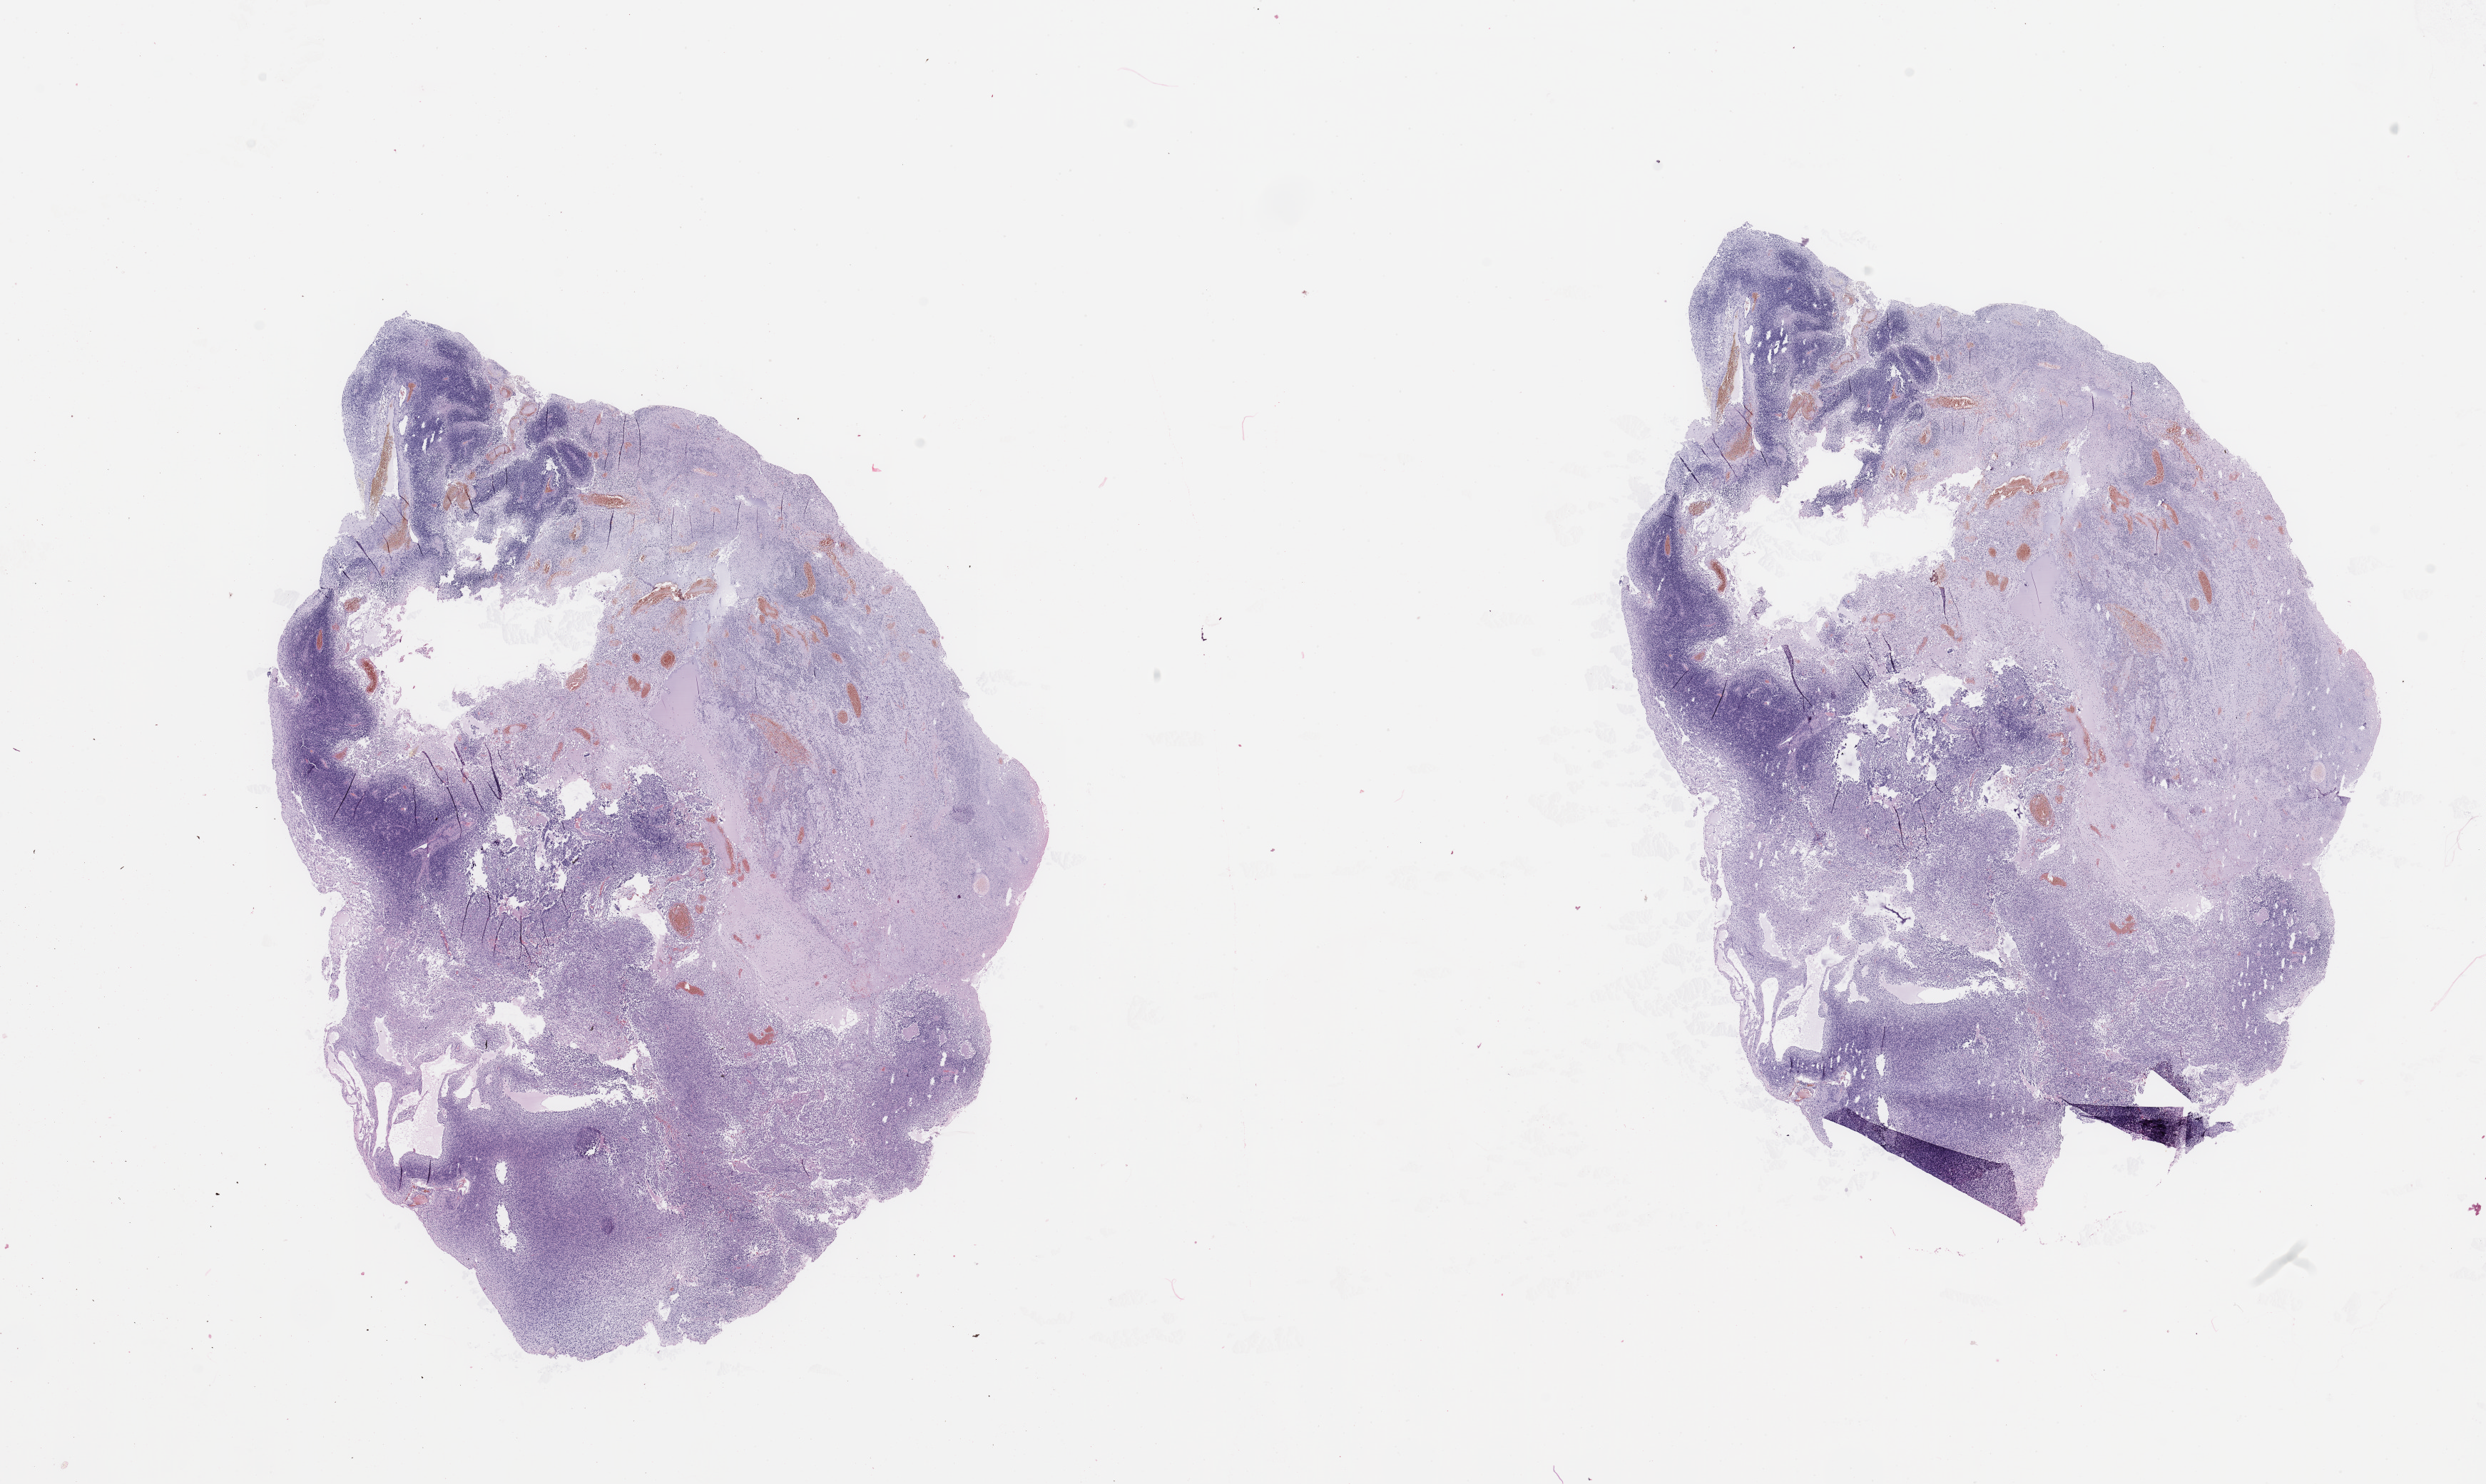
Hematoxylin and eosin (H&E) stained whole-slide image, a low-resolution overview of the entire scanned area, about 27.6 x 16.5 mm, tumour tissue sample, brain. 81-year-old male patient.
Diagnosis: Glioblastoma. Primary tumour site (as recorded): temporal lobe.